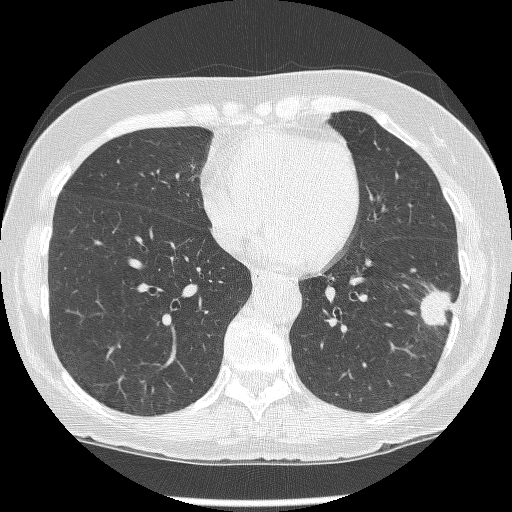
Axial slice from a low-dose chest CT screening exam, baseline annual screen, lung window (W 1500 / L -600 HU), 1.25 mm slice thickness, lung (sharp) reconstruction kernel (BONE), 512 × 512 image matrix, field of view 303 × 303 mm. Female participant, aged 62 years at enrolment. Former smoker at enrolment.
Expert reader's lesion annotation, bounding box (x1, y1, x2, y2) in pixels: (418, 283, 461, 335). The screening reader recorded 2 non-calcified nodules or masses ≥4 mm on this exam (left lower lobe, left lower lobe); which of them this box marks is not recorded. Official screen result: positive, change unspecified: nodule(s) >= 4 mm or enlarging nodule(s), mass(es), or other non-specific abnormalities suspicious for lung cancer. Later outcome: lung cancer diagnosed 15 days after this screen — non-small cell carcinoma, left lower lobe, stage IIIB (AJCC 6th edition), 23 mm at pathology.